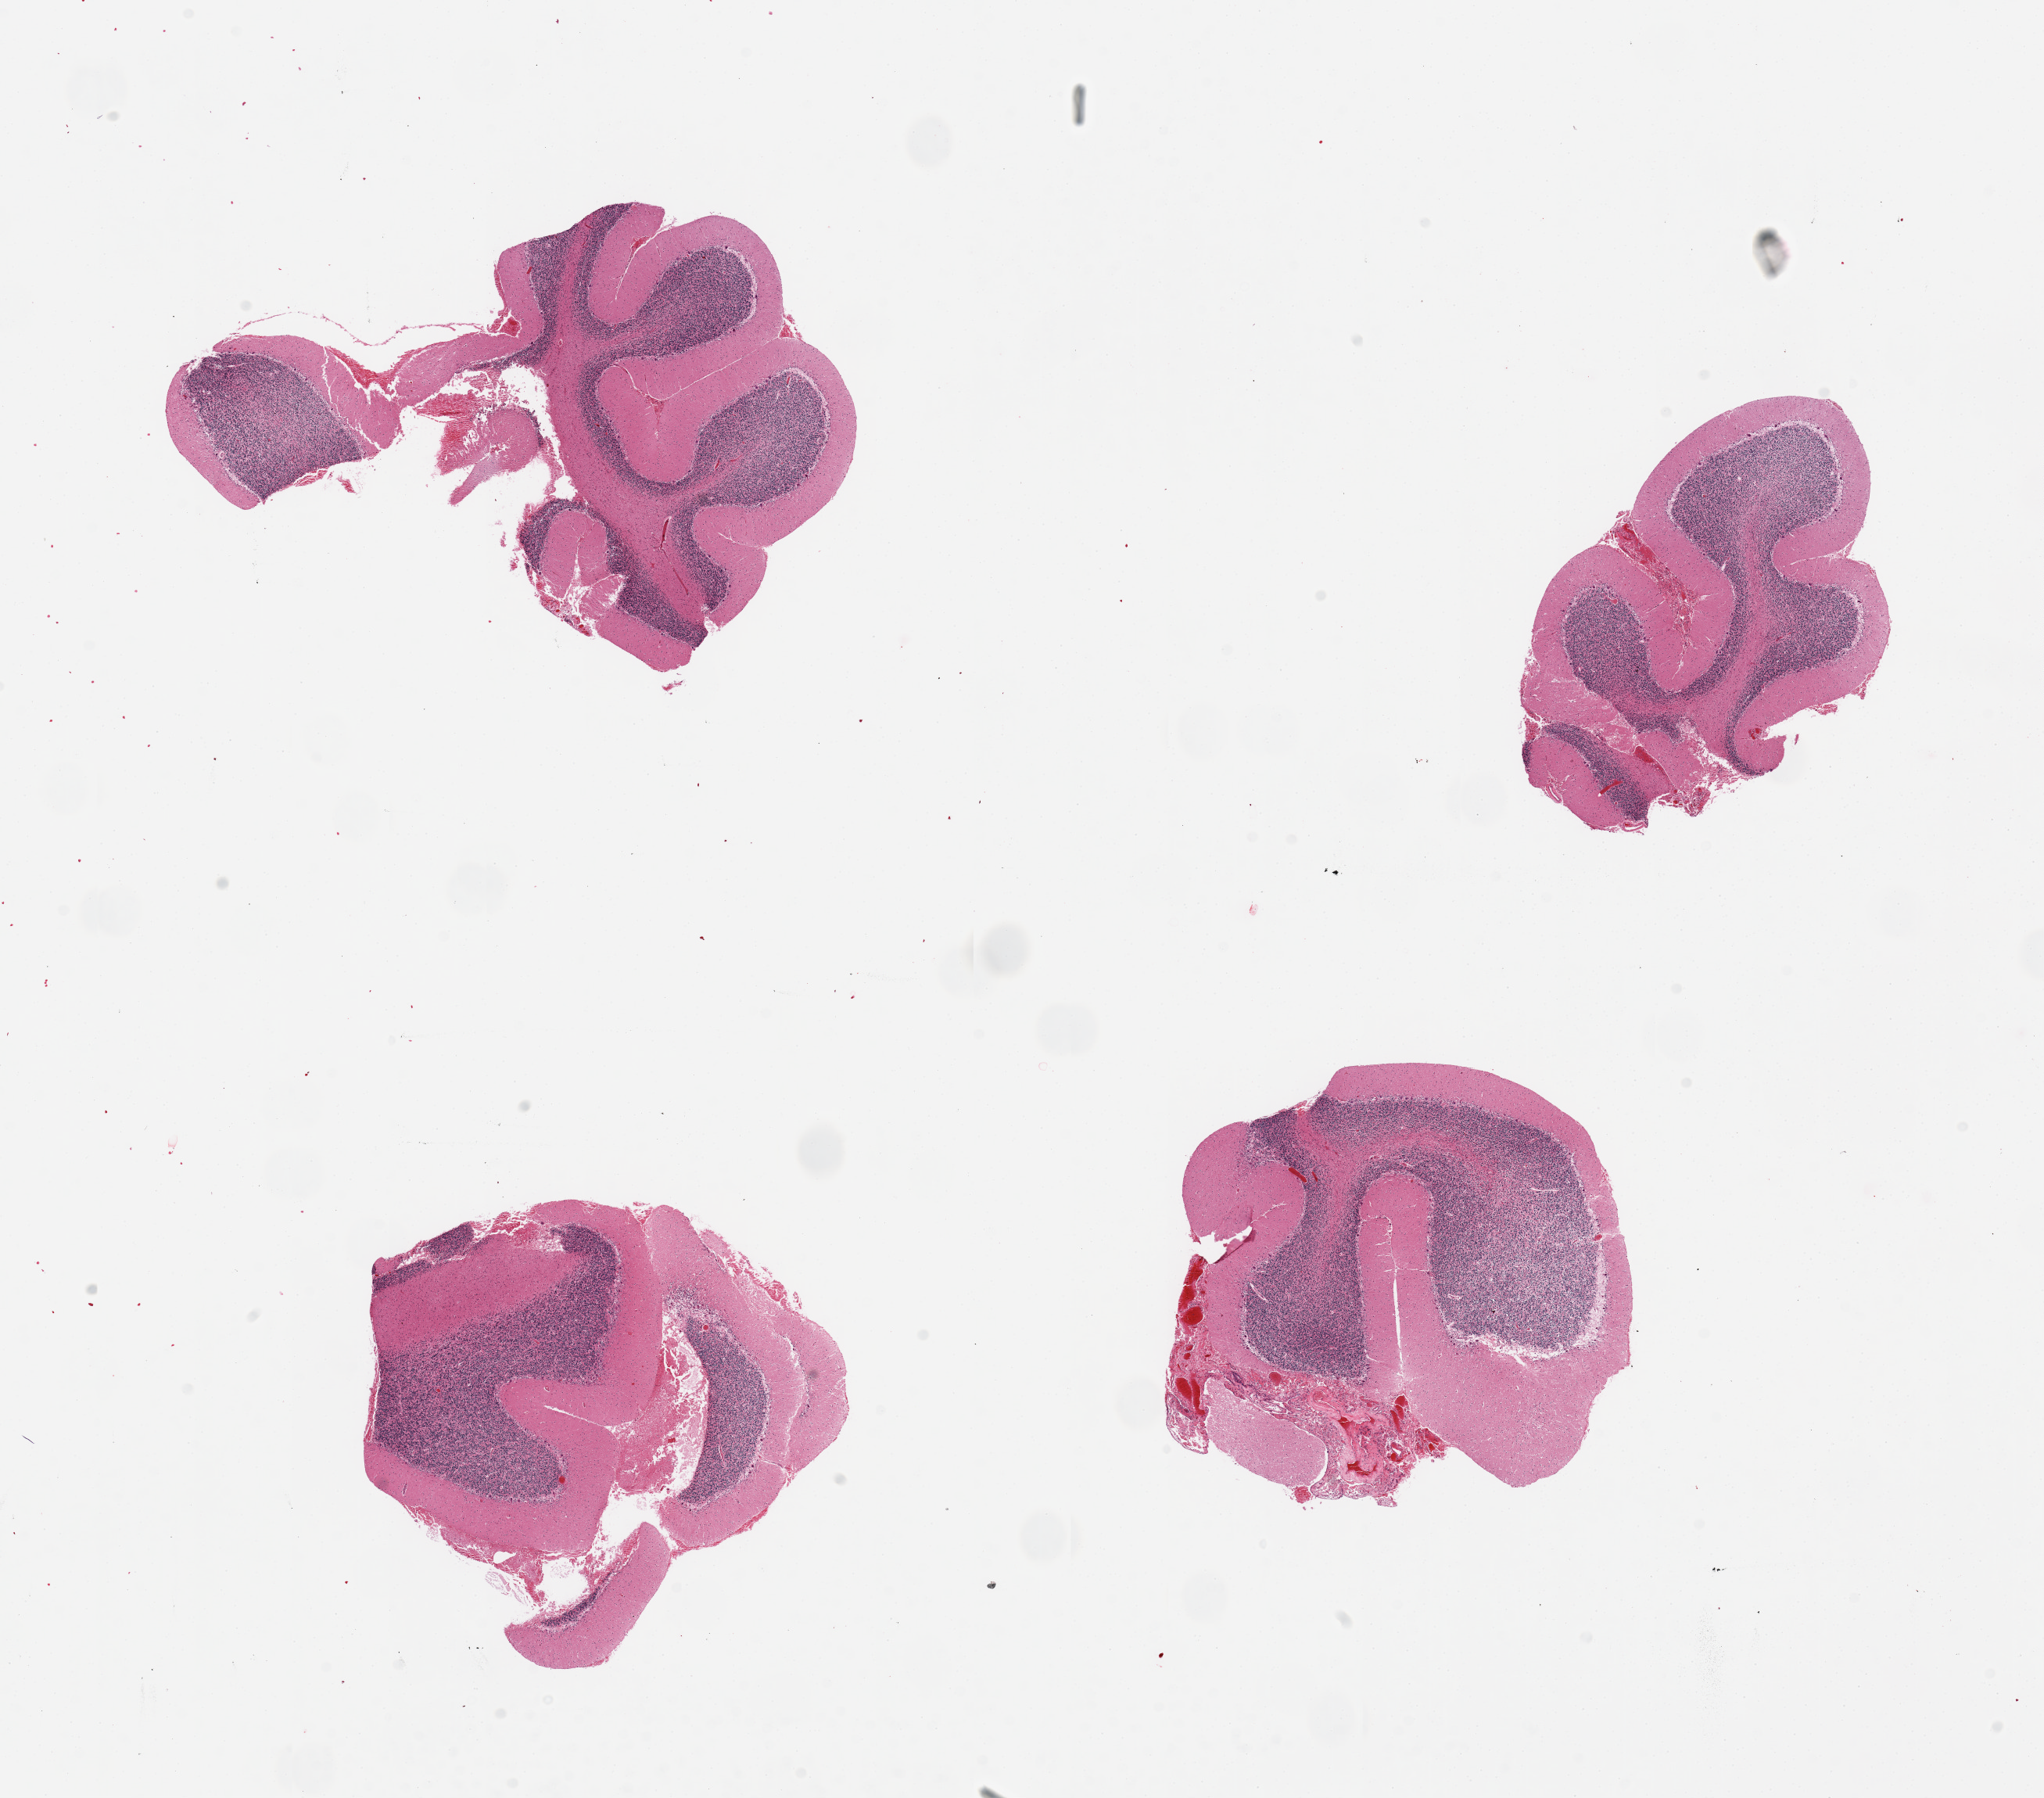
Haematoxylin and eosin whole-slide image — shown as a low-resolution overview of the whole scanned area (about 20.7 x 18.2 mm); PAXgene-fixed, paraffin-embedded tissue; sampled site (target tissue): cerebellum; donor tissue sample. Donor sex: male.
* reviewer comment on this tissue sample: 4 pieces, no significant abnormalities